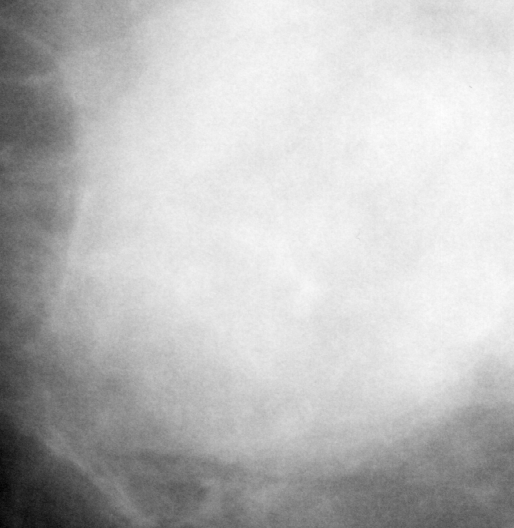
Crop from a digitized film mammogram around one marked abnormality; right breast; CC view; BI-RADS breast density category 4 (scale 1–4).
Finding: mass, shape lobulated, margins obscured; BI-RADS assessment category 3; subtlety rating 4 on a 1 (subtle) to 5 (obvious) scale; pathology (as recorded): benign.